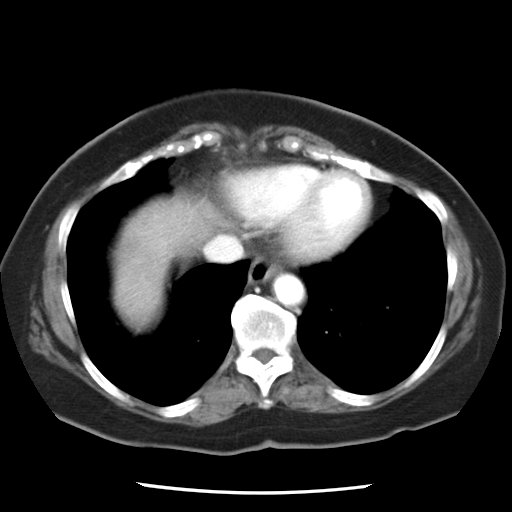
Contrast-enhanced abdominal CT, one axial slice. Position 23 of 24 along the scan axis. 120 kVp. Intravenous contrast given. Soft-tissue window (W 400 / L 40 HU). 512 × 512 image matrix, field of view 312 × 312 mm. Female patient, age 71 years. From the clinical record (not read from this slice): diagnosis: colorectal cancer liver metastases, imaged before liver resection; multiple liver metastases: no; largest metastasis: 4.3 cm; disease in both lobes: no.
Structures marked on this image (outlined manually by an expert reader):
- liver: box from (x=113, y=195) to (x=222, y=327) px
- planned liver remnant (the part of the liver to remain after resection): (x=112, y=195)–(x=219, y=327)